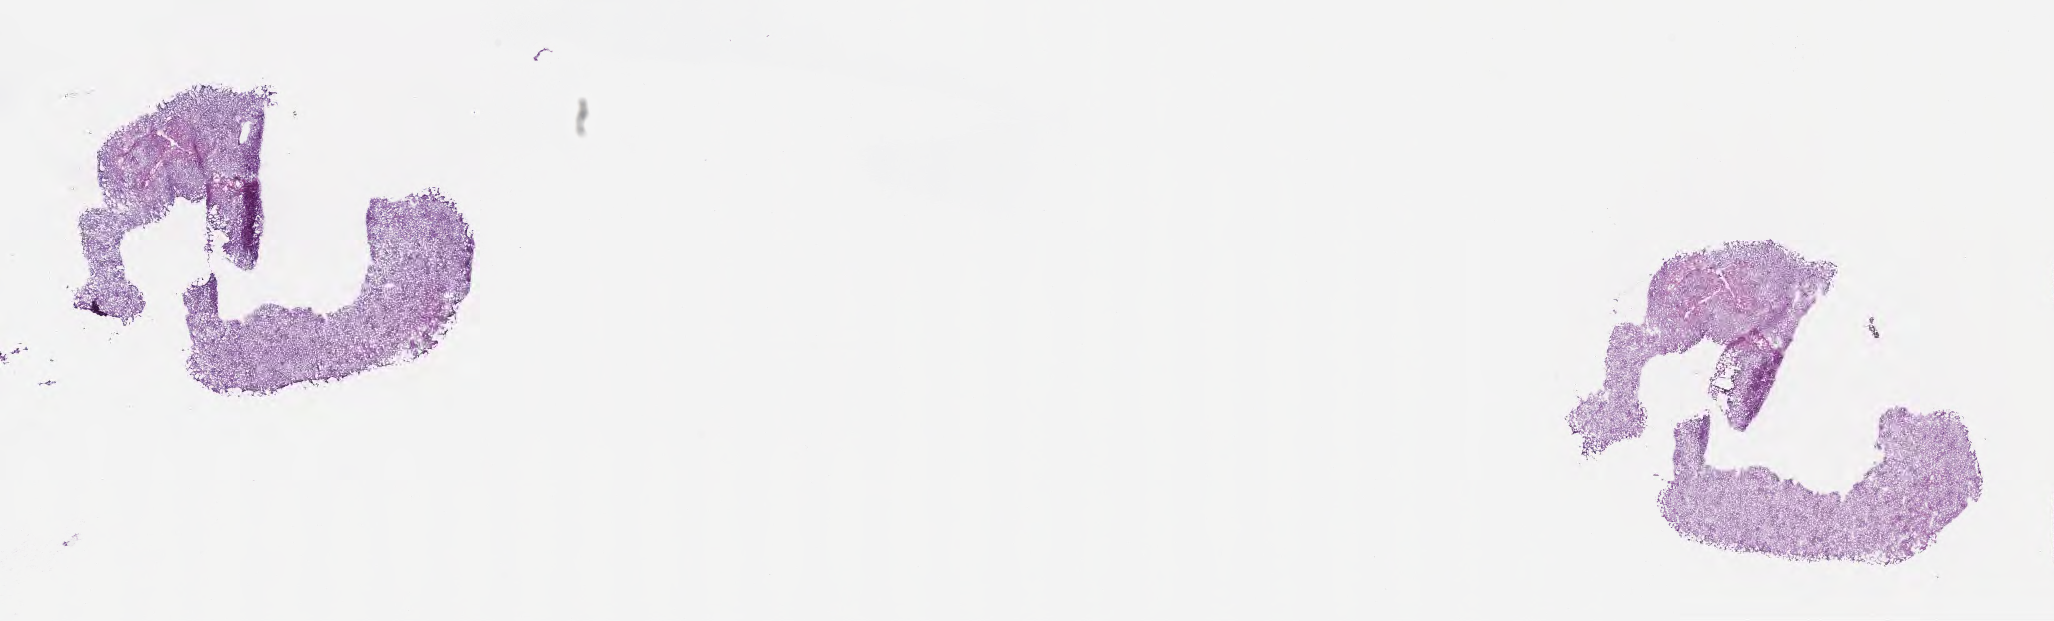
Whole-slide image, haematoxylin and eosin stain — shown as a low-resolution overview of the whole scanned area (about 16.6 x 5.0 mm); frozen section; specimen: primary tumor; anatomic site: brain. Male, age 68 years at initial diagnosis. Slide review estimates, as recorded: tumor cells 38%, tumor nuclei 74%, stromal cells 49%, necrosis 0%, normal cells 13%. Infiltration values recorded for this section: lymphocyte infiltration 0%, monocyte infiltration 0%, neutrophil infiltration 0%.
Section: bottom of the tissue portion. Histologic diagnosis: Glioblastoma, NOS.